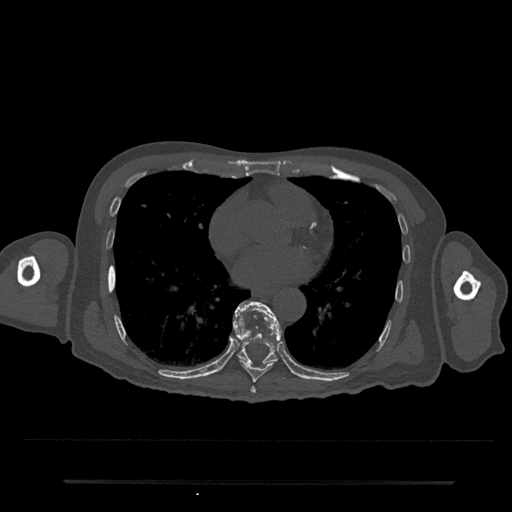
CT including the spine, one axial slice; position 399 of 797 along the scan axis; reconstruction kernel Br40s/3; bone window (W 1800 / L 400 HU); 512 × 512 image matrix. Male patient, age 74 years. From the clinical record (not read from this slice): primary cancer: prostate.
Outlined on this slice (semi-automatically segmented with operator editing):
- T7 vertebra: box from (x=250, y=386) to (x=256, y=394) px
- T8 vertebra: (x=233, y=301)–(x=279, y=383)
- T9 vertebra: (x=233, y=301)–(x=282, y=364)